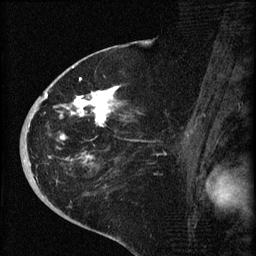
Breast MRI (dynamic contrast-enhanced), one sagittal slice. Slice 35 of 60 in the series (ordered by position). Dynamic contrast-enhanced series, image 2 of 4 at this slice position (ordered by acquisition). 1.5 T. TE 4.2 ms, TR 8.2 ms. 256 × 256 image matrix, field of view 180 × 180 mm. Patient: female, 71 years.
Annotated regions visible in this slice (semi-automatic segmentation, software-assisted and operator-edited):
- analysis volume of interest (the breast-tissue region the enhancement analysis was run in; not a lesion): bounding box <35,75,143,190> (left, top, right, bottom; pixels)
- tumour enhancement mask (voxels above the 70 % enhancement threshold inside the analysis volume of interest): <44,77,121,165>